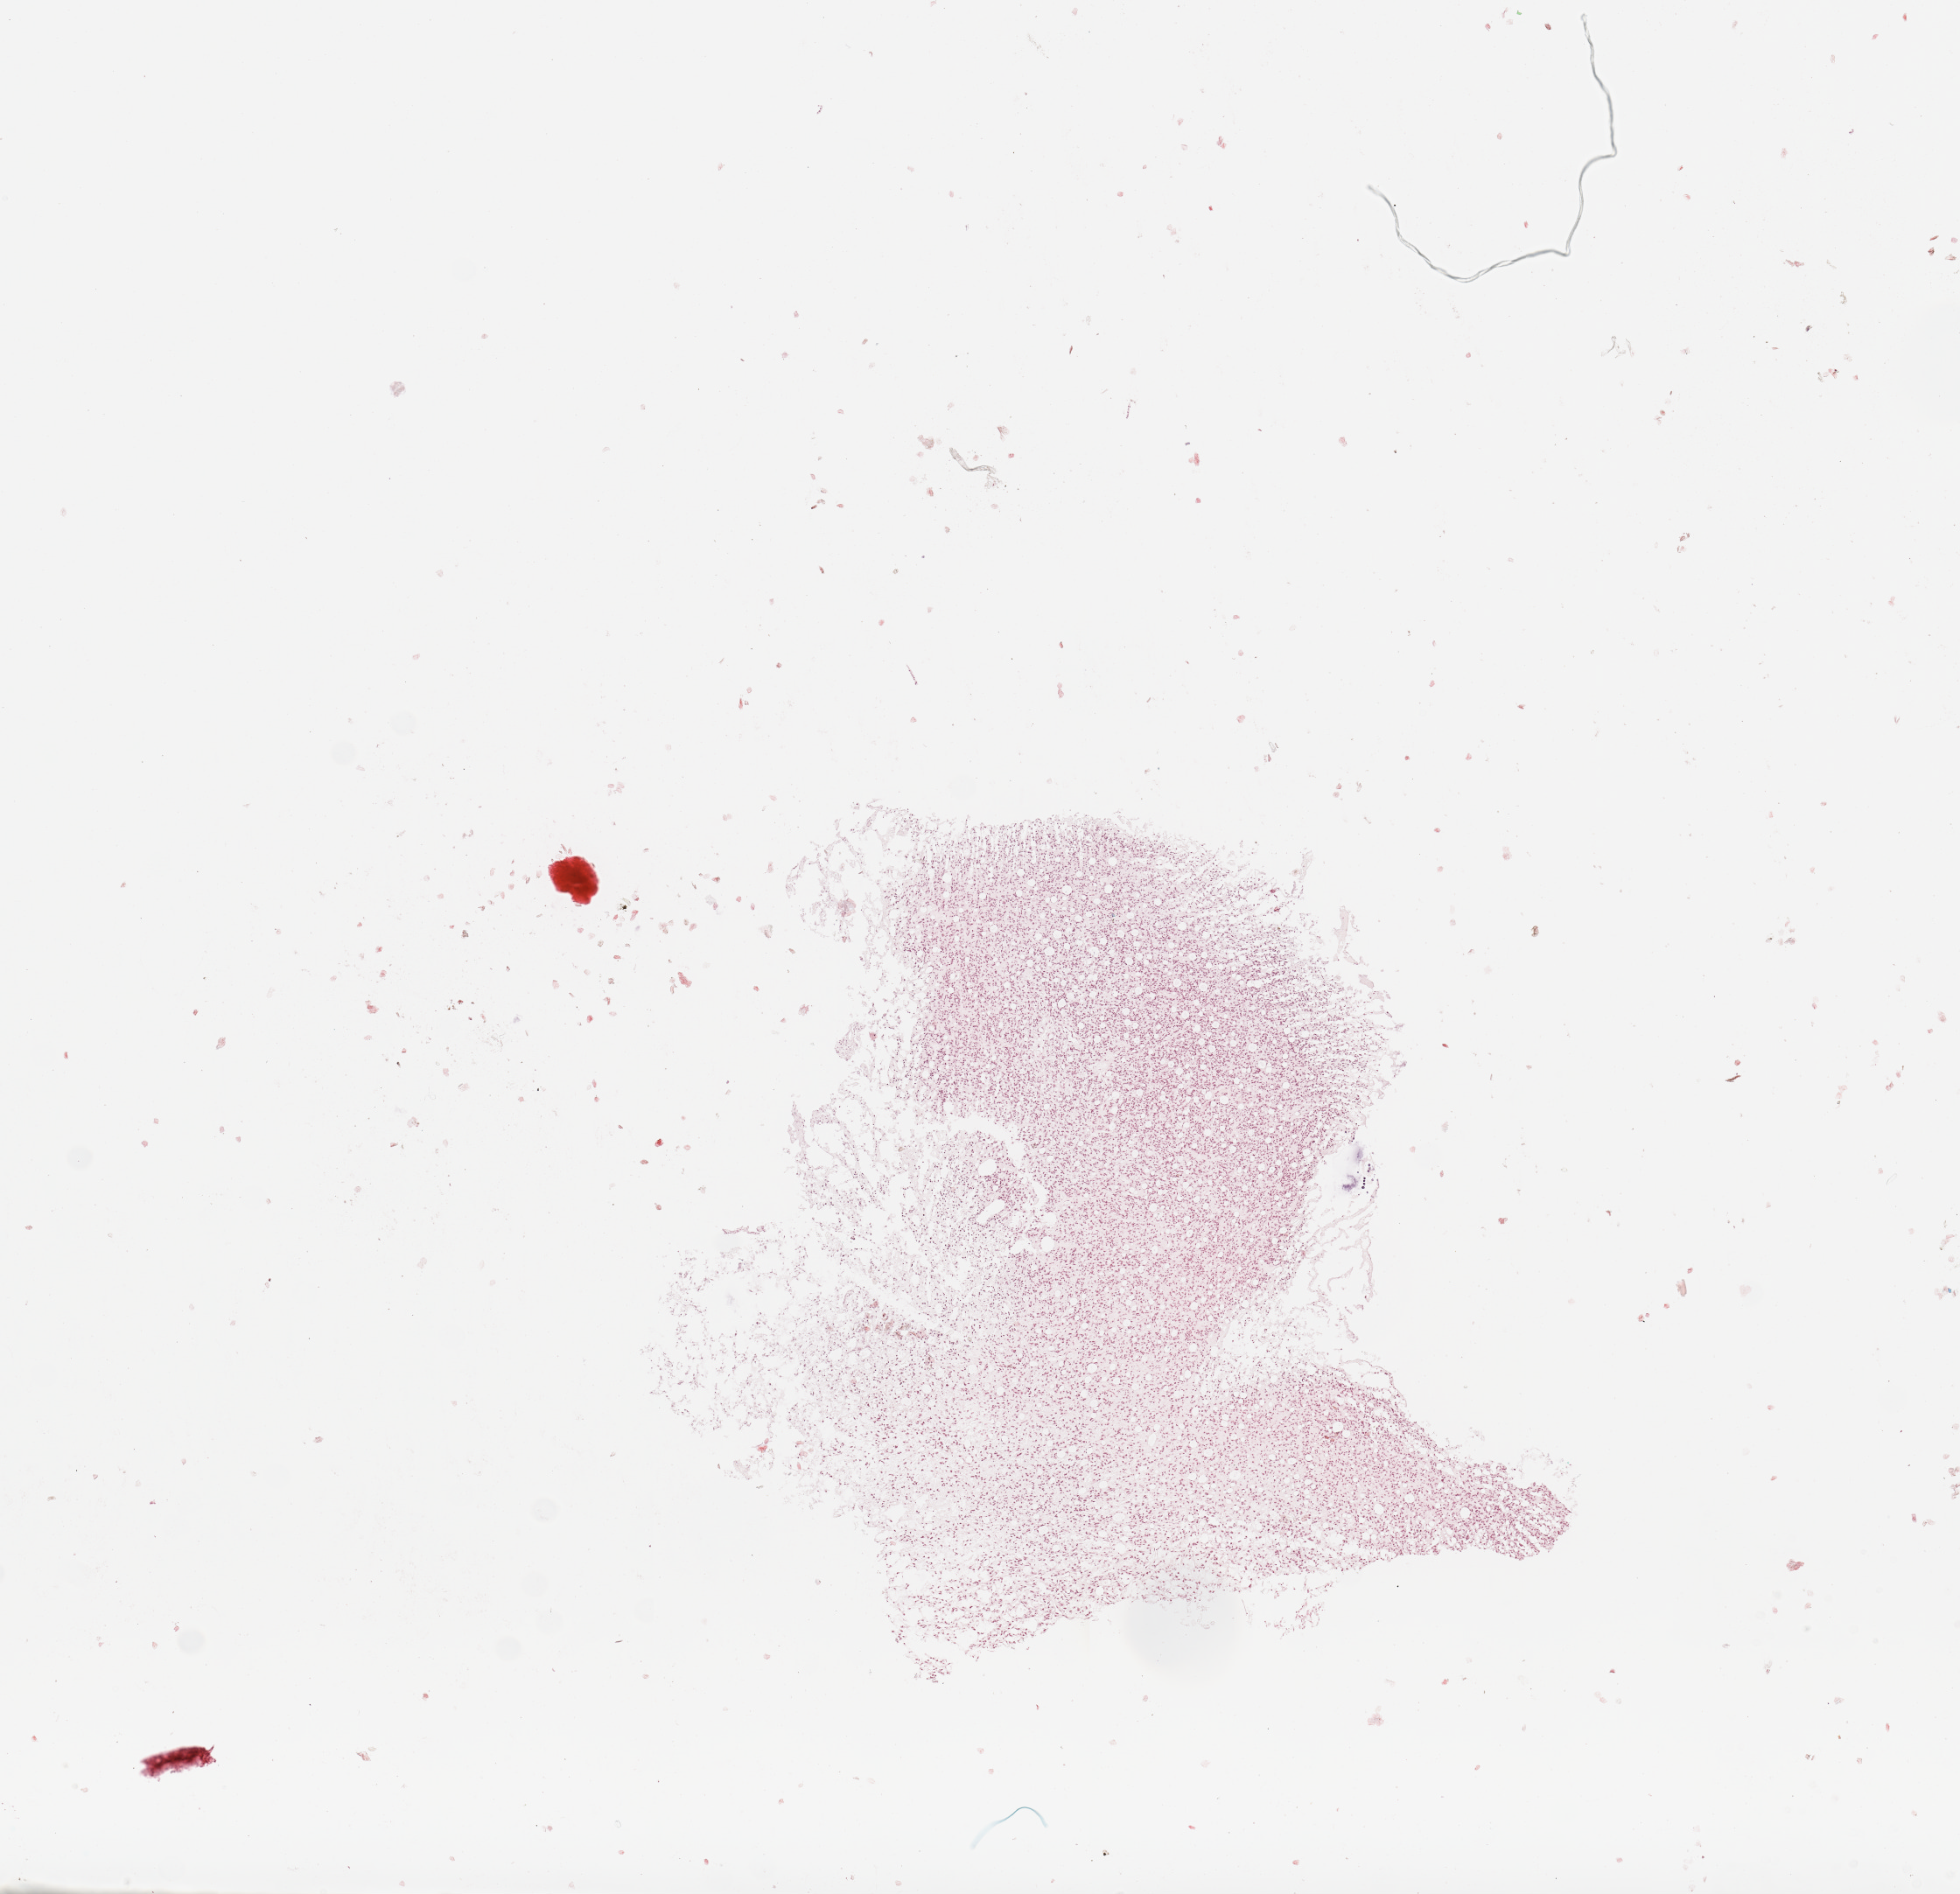
Digitized Hematoxylin and eosin (H&E) stained tissue section (whole slide), a low-resolution overview of the entire scanned area, about 8.9 x 8.6 mm; tumour tissue sample, sampled site: frontal lobe. 52-year-old female patient. Composition of this section per pathologist review: tumour nuclei 90%, necrosis 5%.
• primary tumour site (as recorded): frontal lobe
• diagnosis: Glioblastoma